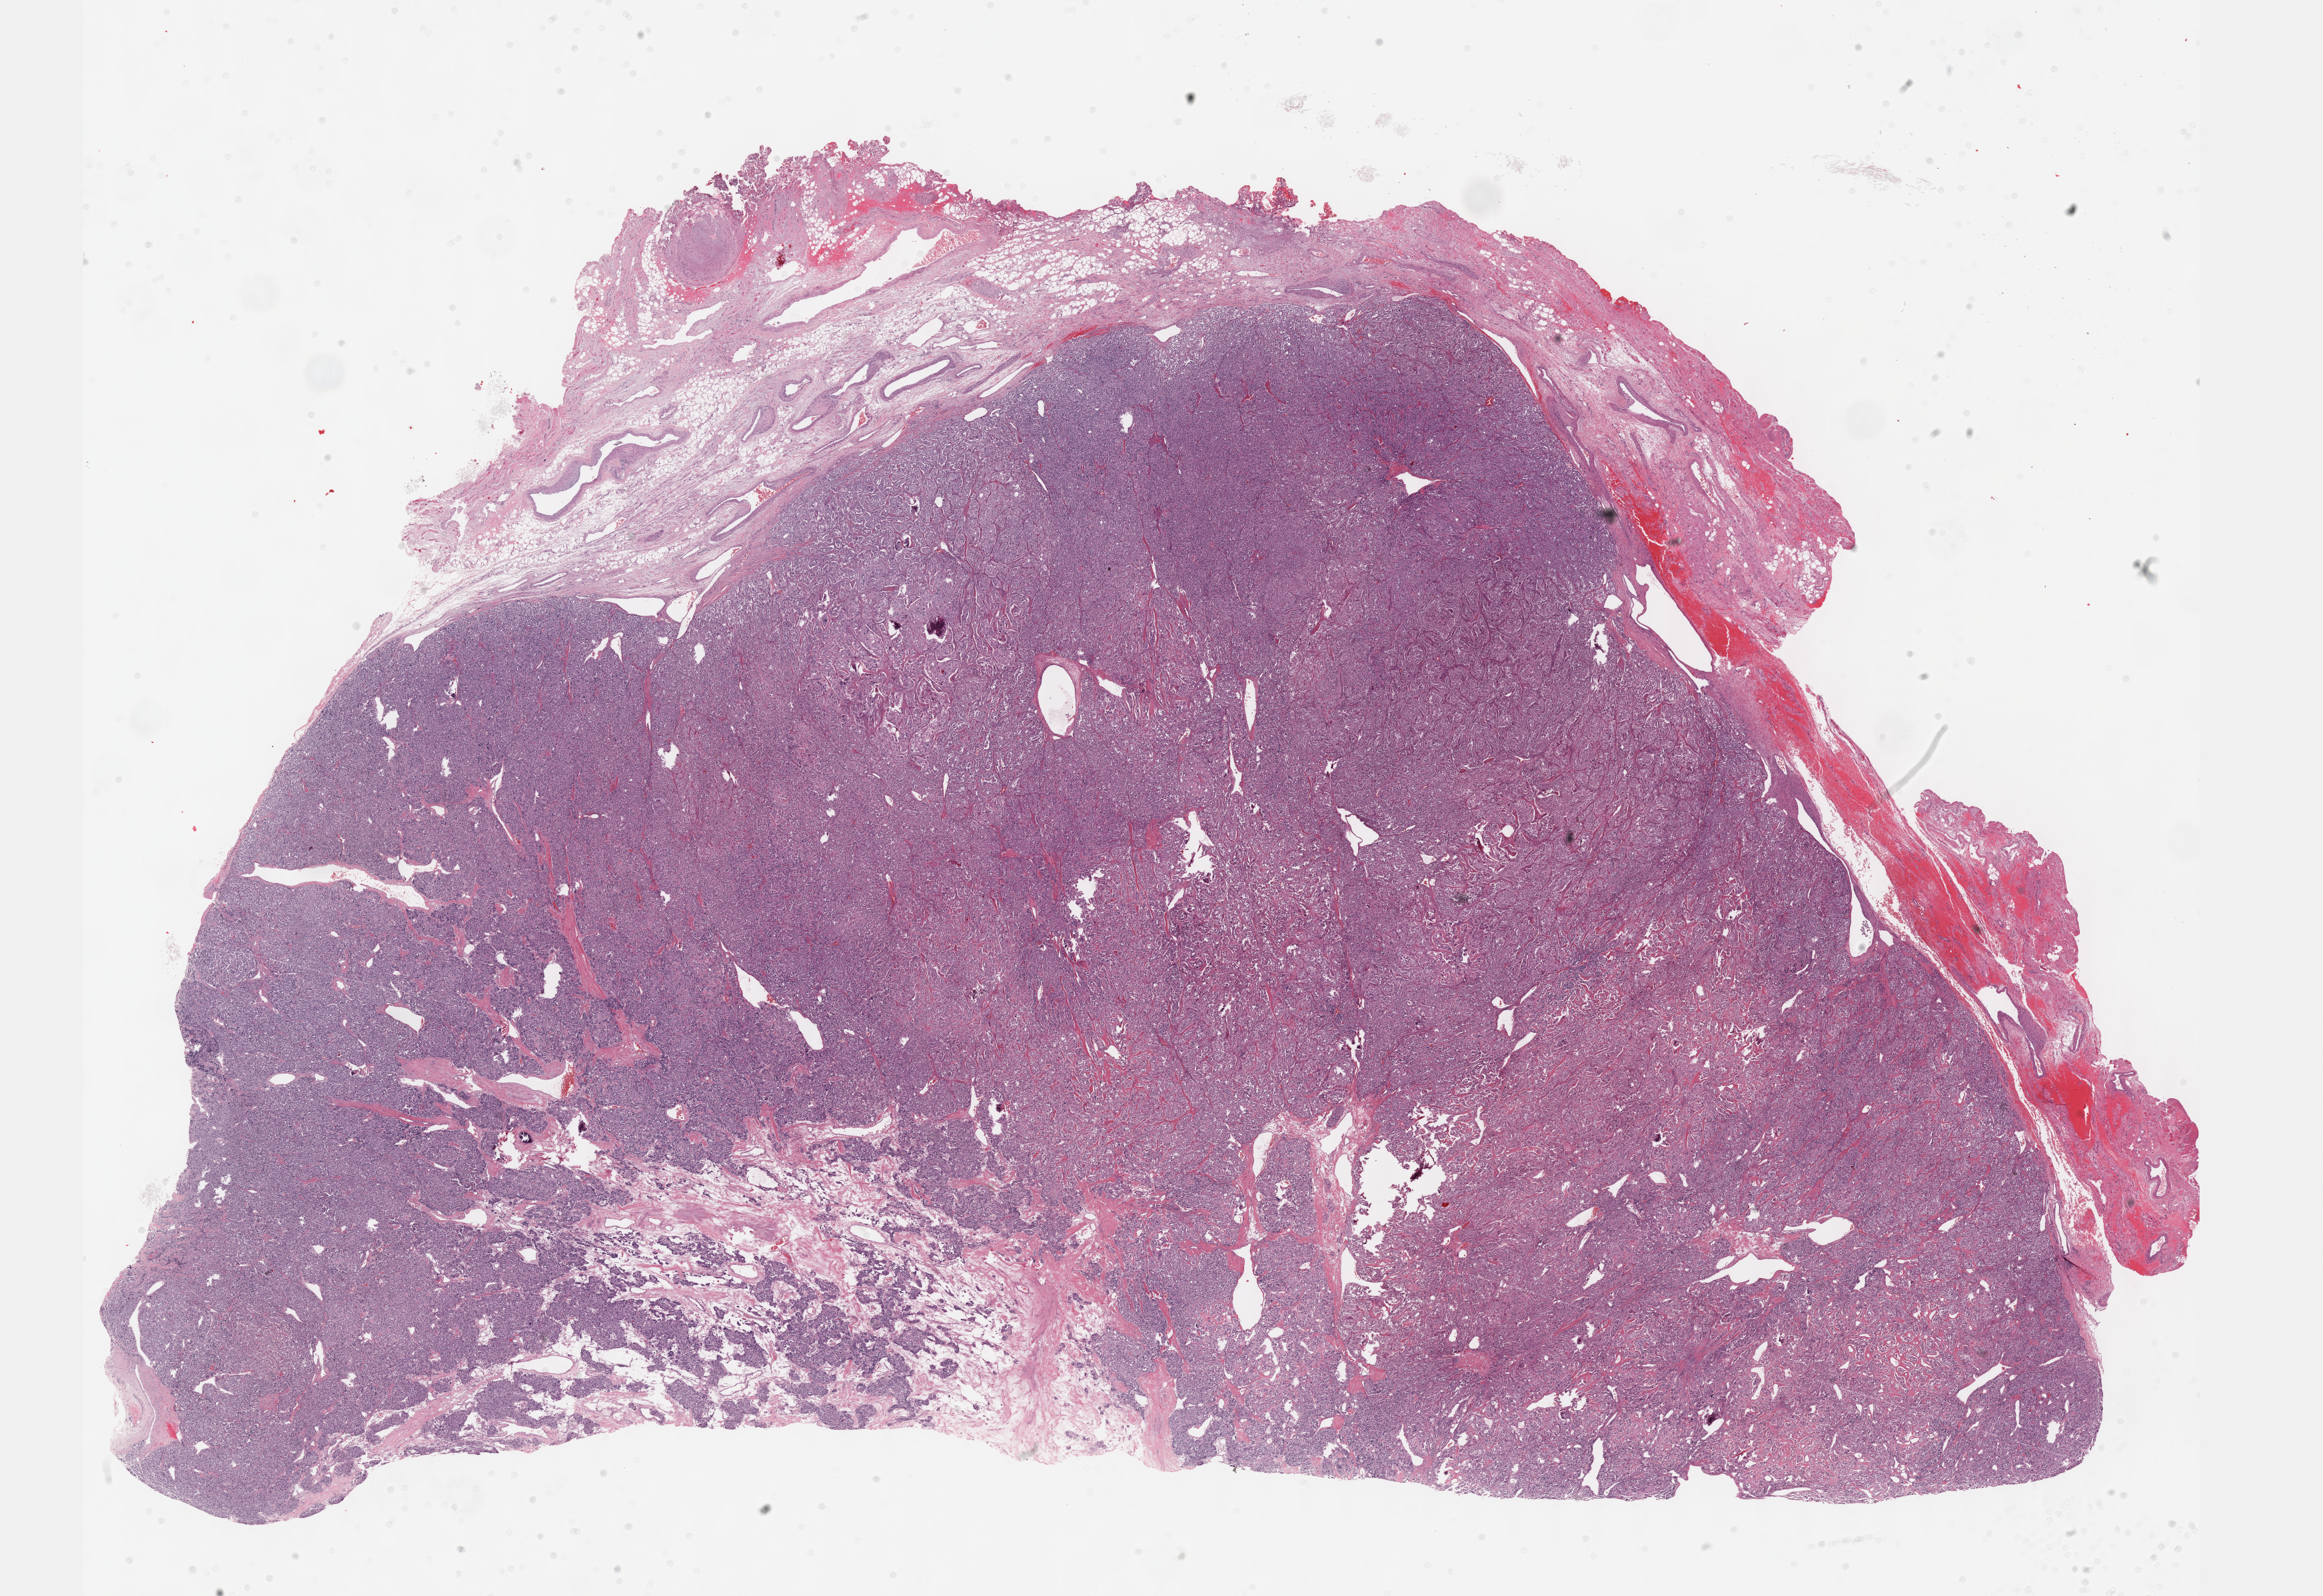
Digitized H&E tissue section (whole slide), shown as a low-resolution overview of the whole scanned area (about 28.2 x 19.4 mm, acquisition: 40x scan), formalin-fixed paraffin-embedded (FFPE) diagnostic section, sample: primary tumour, heart, mediastinum, and pleura. Patient: female, age at initial diagnosis 63 years.
Lymph nodes positive (case pathology): 0 of 3 examined. Diagnosis: Extra-adrenal paraganglioma, NOS.